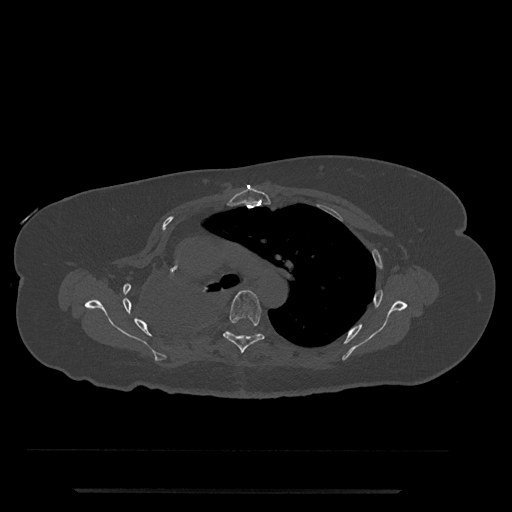
CT including the spine, one axial slice; slice 541 of 797 in the series (ordered by position); bone window (W 1800 / L 400 HU); 512 × 512 image matrix, field of view 440 × 440 mm. Female patient, age 51 years. Case-level facts recorded for this patient, not image findings: primary cancer: neuro.
Outlined on this slice (semi-automatically segmented with operator editing):
- T5 vertebra: bounding box <223,290,265,353> (left, top, right, bottom; pixels)
- T6 vertebra: <227,331,257,335>